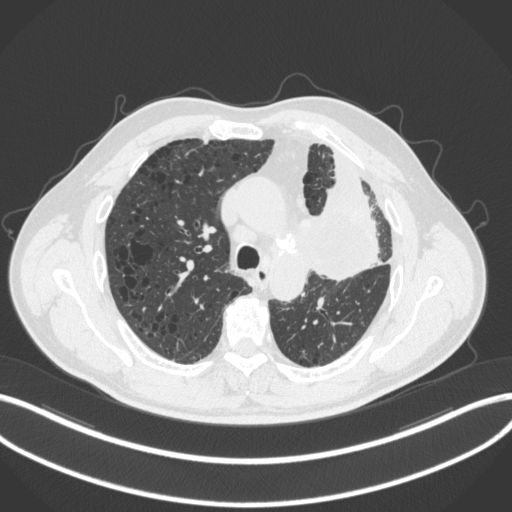
Chest CT, one axial slice. Position 203 of 286 along the scan axis. Reconstruction kernel B31f. 120 kVp. Lung window (W 1500 / L -600 HU). 512 × 512 image matrix, field of view 400 × 400 mm. Male patient, age 68 years. From the clinical record (not read from this slice): clinical TNM (as recorded): T3 N3 M1.
Structures marked on this image (bounding box drawn by a radiologist):
- lung tumour (recorded histology: adenocarcinoma): bounding box (x1, y1, x2, y2) in pixels: (310, 173, 389, 285)